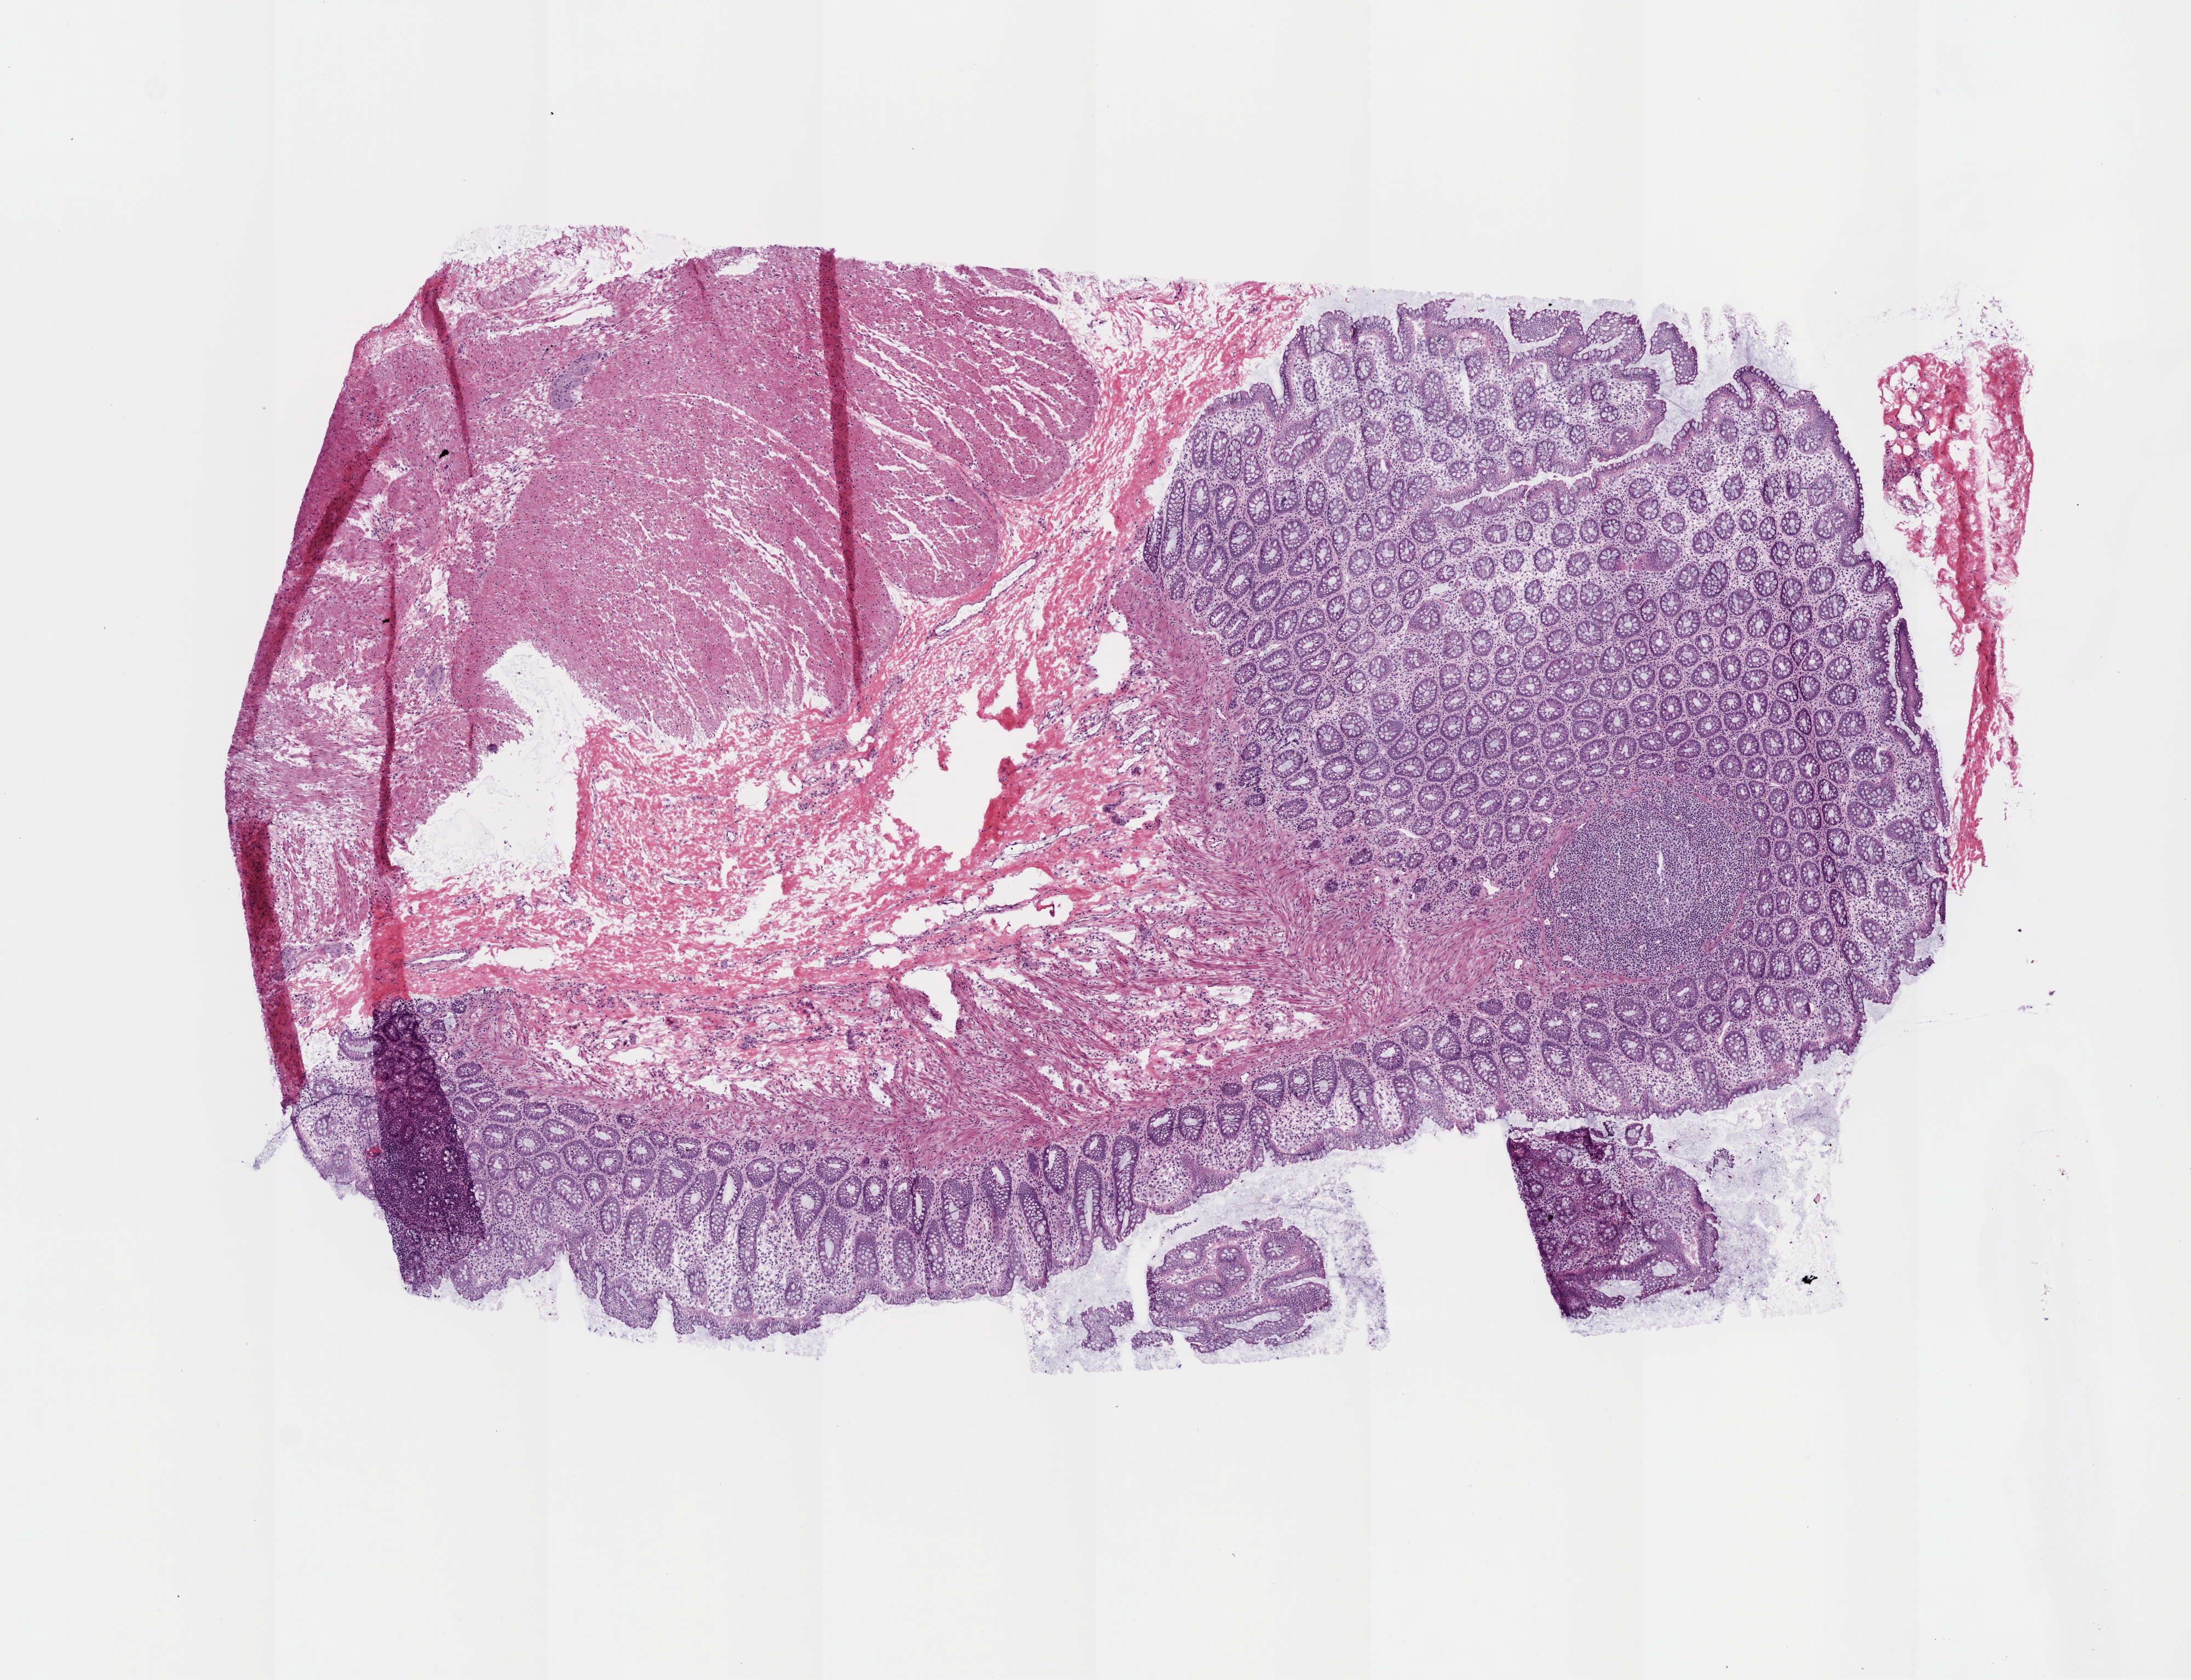
Digitized Hematoxylin and eosin (H&E) stained tissue section (whole slide) — shown as a low-resolution overview of the whole scanned area (about 8.0 x 6.2 mm); frozen section; solid tissue normal (non-tumour tissue) sample from the rectum. Patient: female, age at initial diagnosis 41 years.
This section: solid tissue normal (non-tumour) sample from the same patient. Patient diagnosis: Adenocarcinoma, NOS.